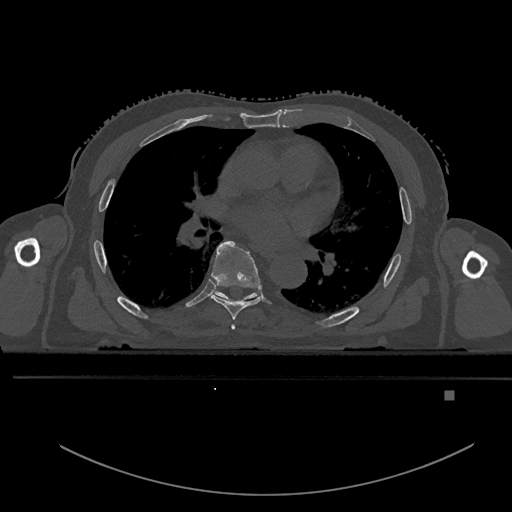
CT including the spine, one axial slice; position 293 of 969 along the scan axis; bone window (W 1800 / L 400 HU); 0.5 mm slice thickness; 512 × 512 image matrix, field of view 456 × 456 mm. Patient: male, 82 years. Case-level facts recorded for this patient, not image findings: primary cancer: prostate.
Structures marked on this image (semi-automatic segmentation, software-assisted and operator-edited):
- T5 vertebra: bounding box [x1, y1, x2, y2] px = [231, 324, 235, 330]
- T6 vertebra: [210, 241, 261, 320]
- T7 vertebra: [214, 291, 256, 299]